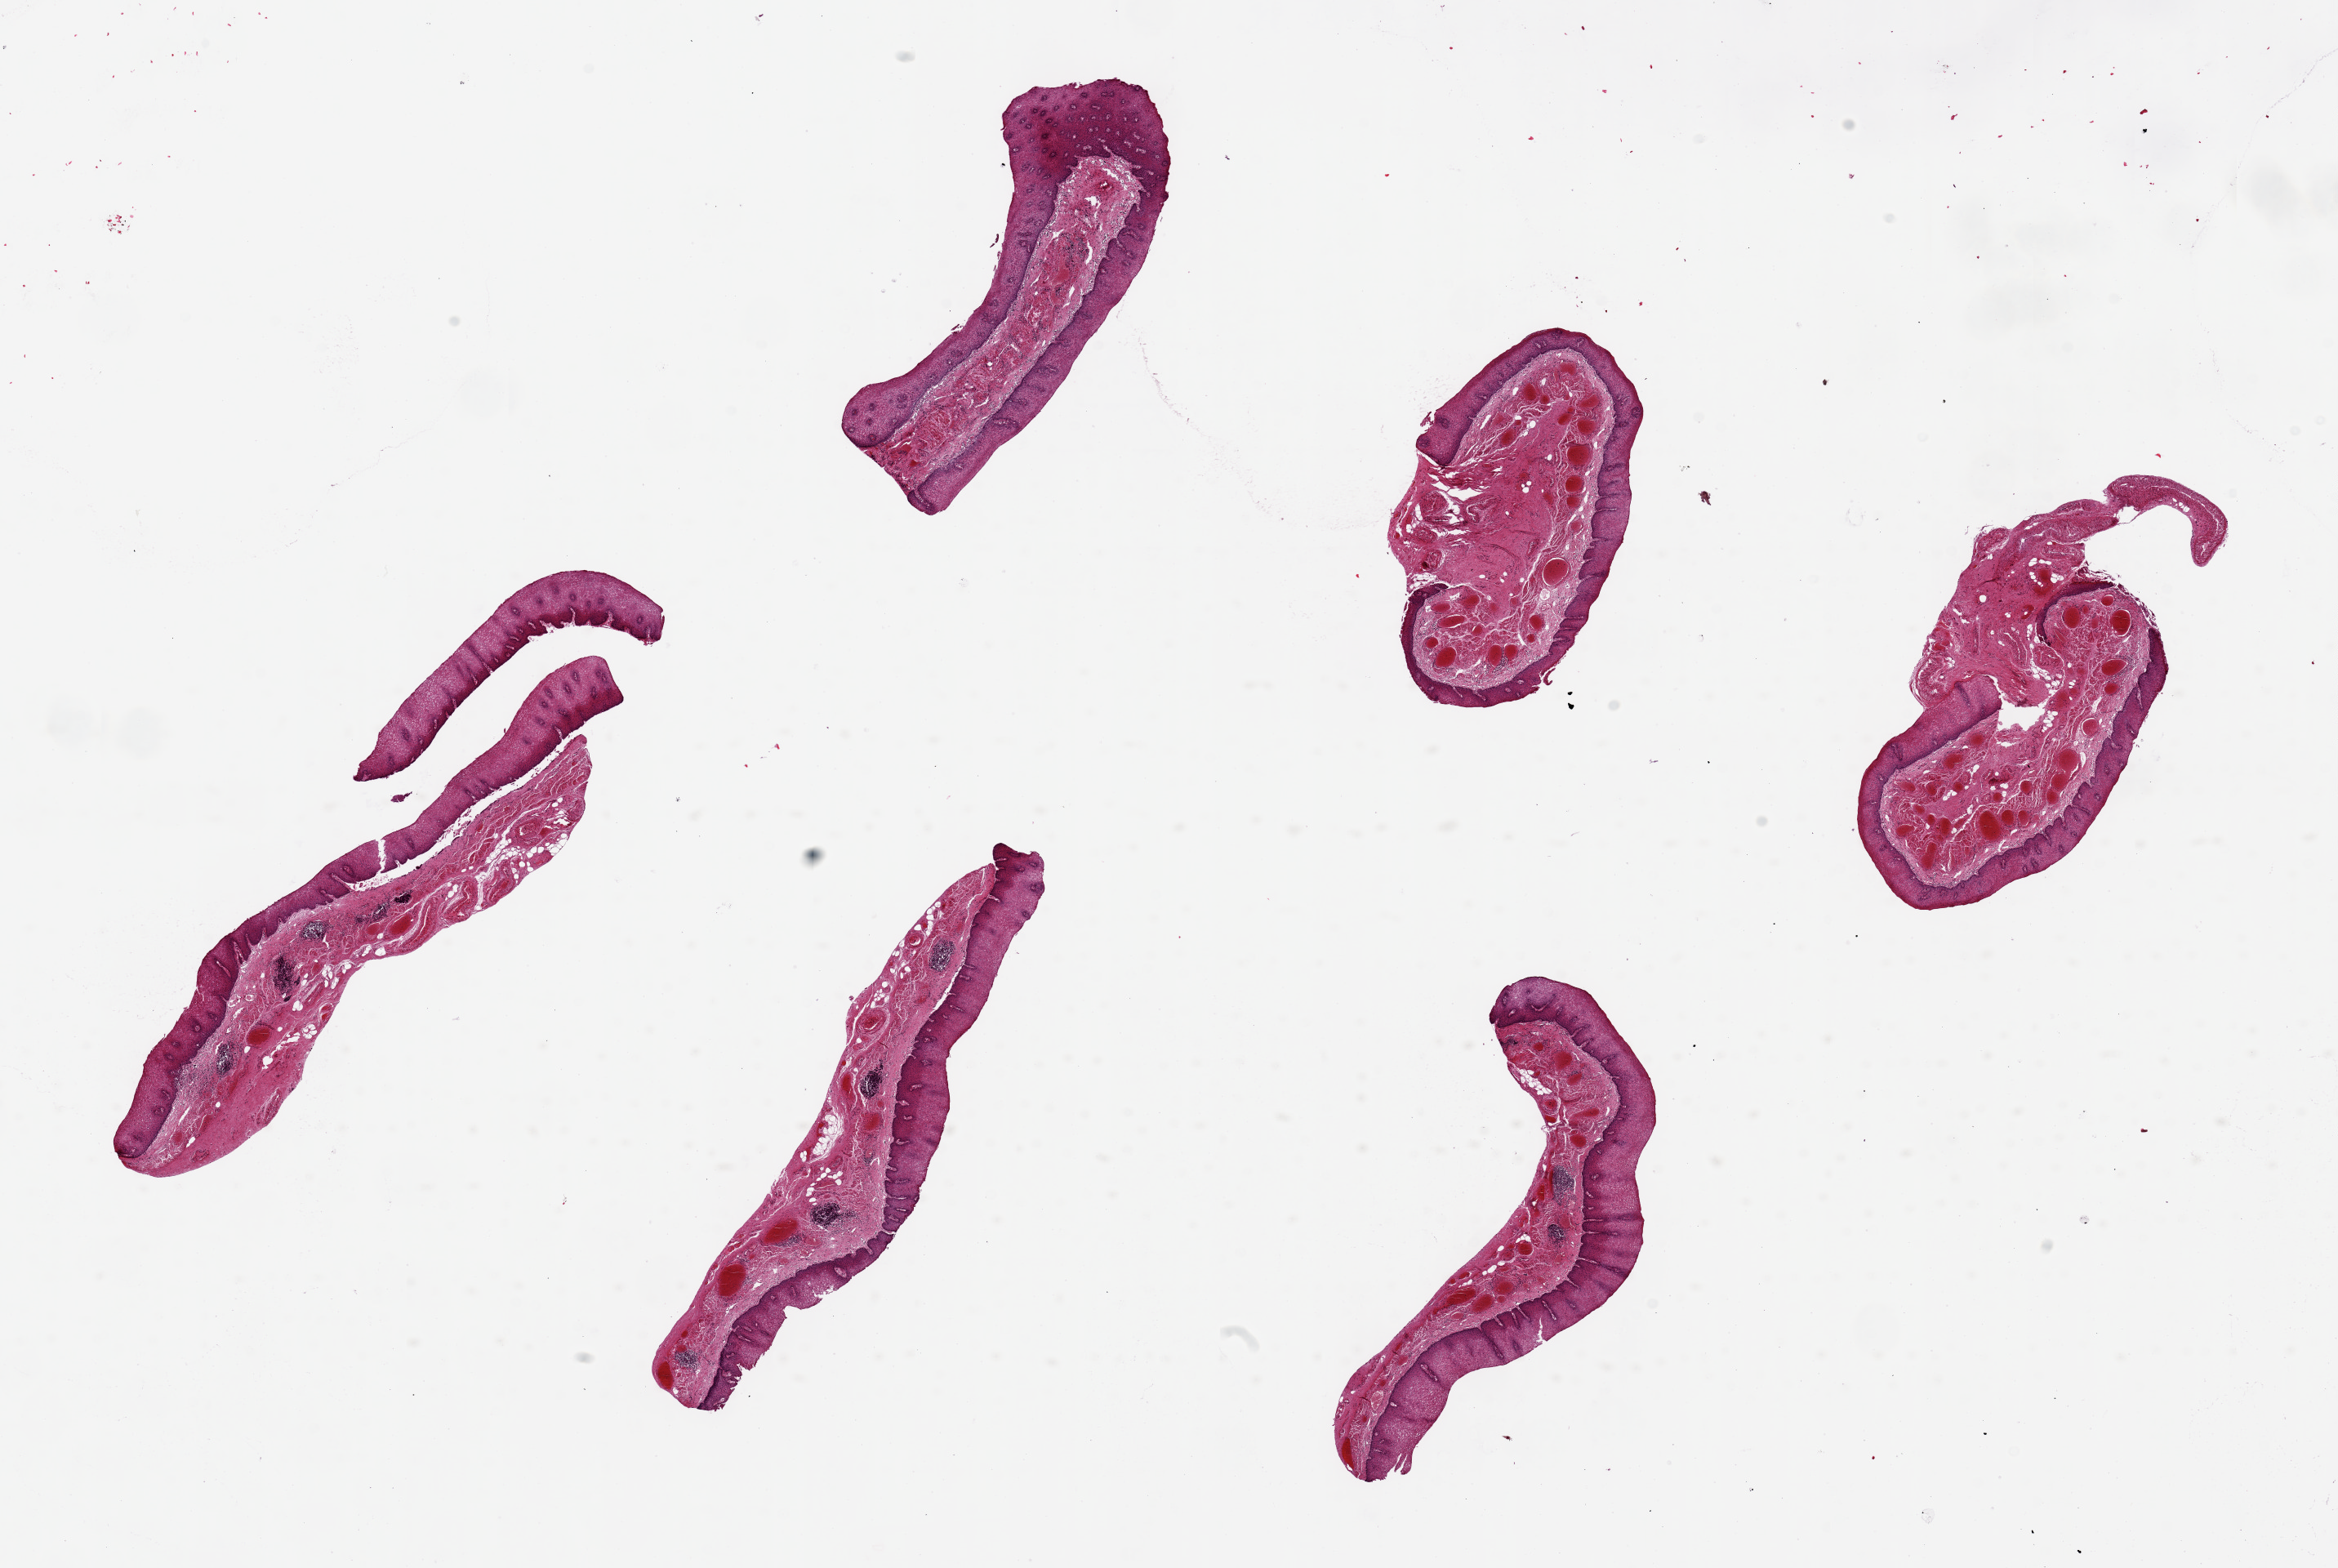
Whole-slide image, haematoxylin and eosin stain, brightfield — shown as a low-resolution overview of the whole scanned area (about 22.6 x 15.2 mm, from a 20x scan). PAXgene-fixed paraffin-embedded (PFPE) section. Target tissue: gastroesophageal junction. Donor tissue sample. Male donor.
Pathologist's review note for this sample: 6 pieces ~5x2mm, 20--50% muscle, squamous mucosa present.